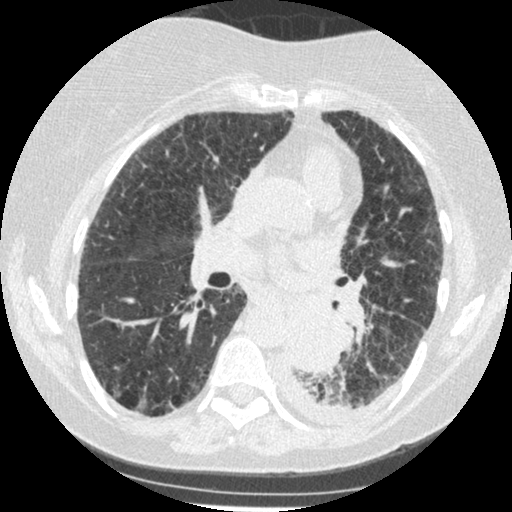
Low-dose screening chest CT, one axial slice. Position 132 of 341 along the scan axis. Reconstruction kernel STANDARD. Lung window (W 1500 / L -600 HU). 1.25 mm slice thickness. 512 × 512 image matrix, field of view 310 × 310 mm.
Outlined on this slice (manually delineated by an expert):
- lesion 1 (tumor, lower lobe of left lung): bounding box (x1, y1, x2, y2) in pixels: (286, 307, 344, 375)